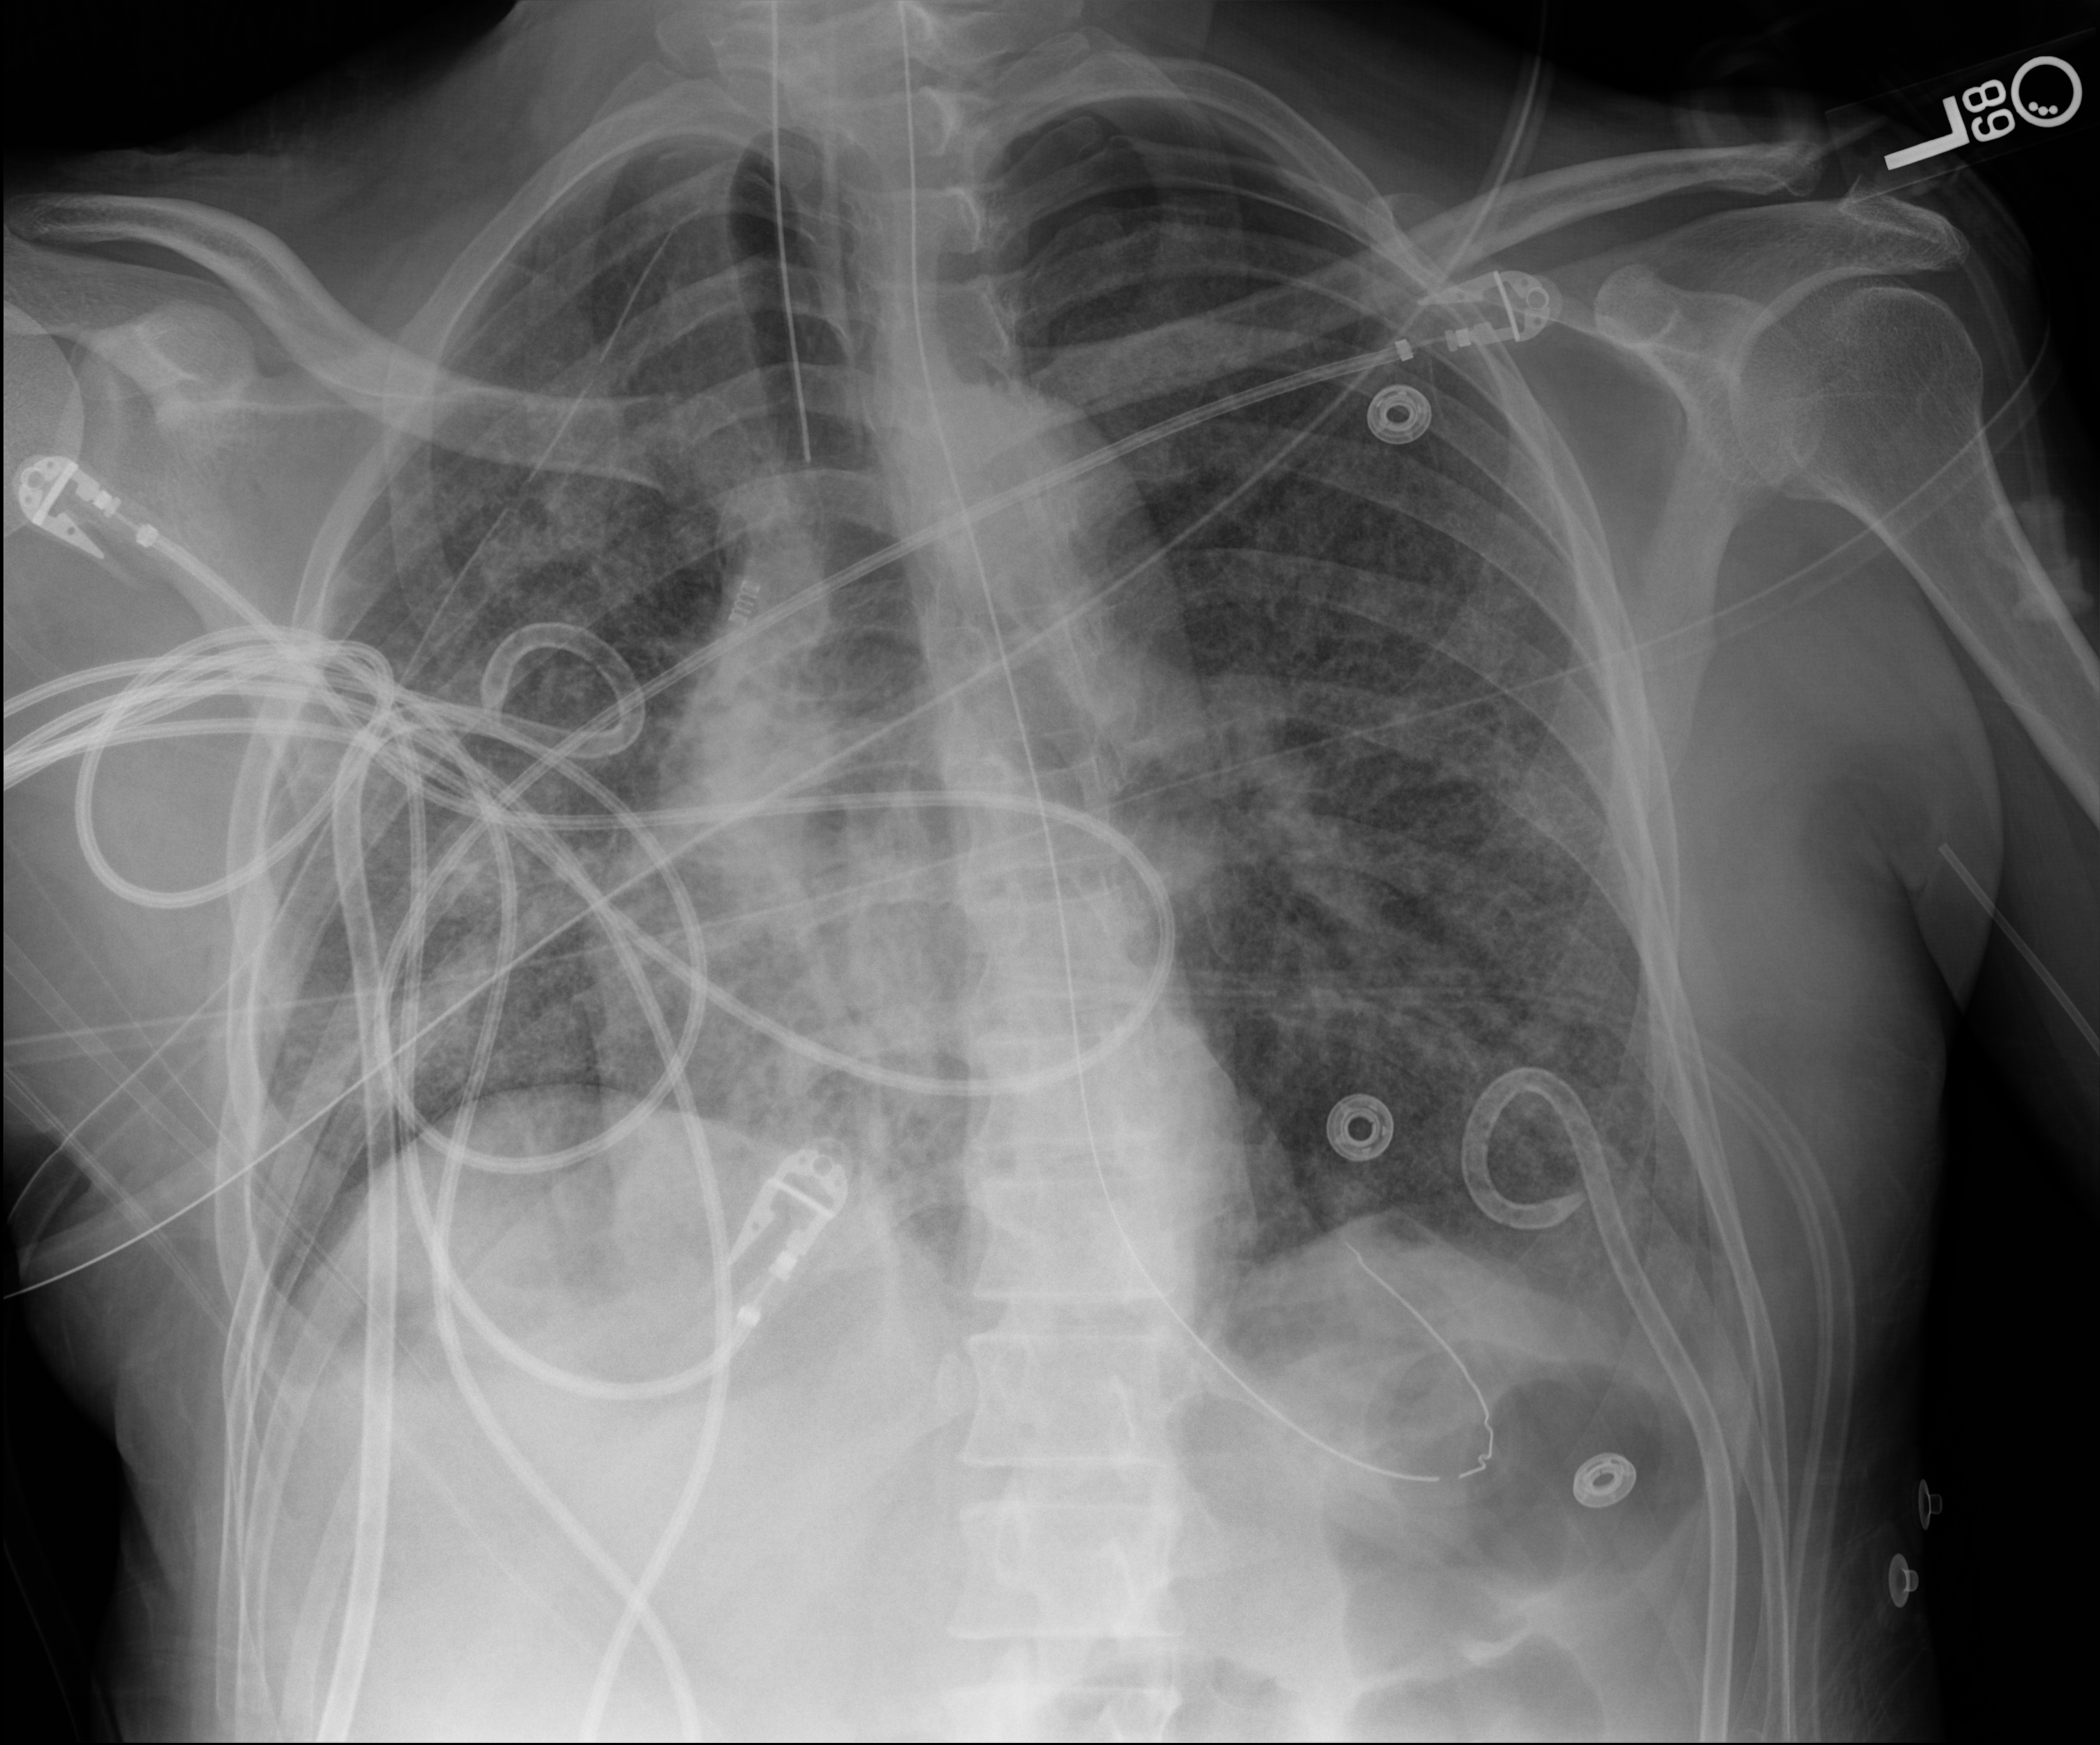
Bedside chest radiograph (digital radiography). Patient hospitalised with COVID-19, aged 18–59 years.
Hospital-stay facts (about this admission, not read from this image; timing relative to this image not recorded):
- admitted to intensive care during this hospital stay: yes
- other chronic lung disease (admission record): no
- mechanically ventilated during this hospital stay: yes